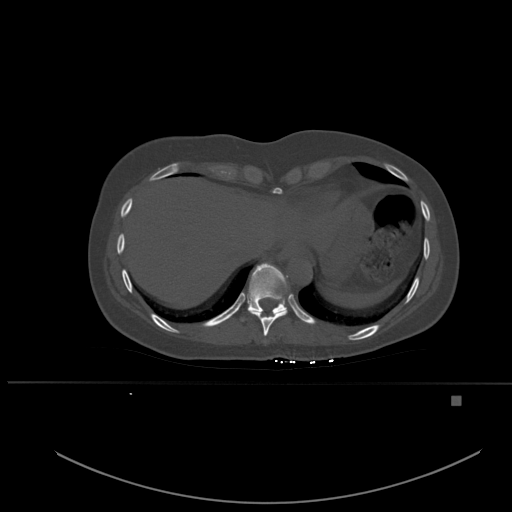
CT including the spine, one axial slice; position 298 of 651 along the scan axis; bone window (W 1800 / L 400 HU); 1.5 mm slice thickness; 512 × 512 image matrix. Patient: female, 49 years. Case-level facts recorded for this patient, not image findings: primary cancer: breast; vertebrae with lytic lesions (as recorded): L3, T12, L4.
Outlined on this slice (semi-automatic segmentation, software-assisted and operator-edited):
- T10 vertebra: box from (x=242, y=263) to (x=287, y=321) px
- T9 vertebra: (x=247, y=276)–(x=288, y=336)